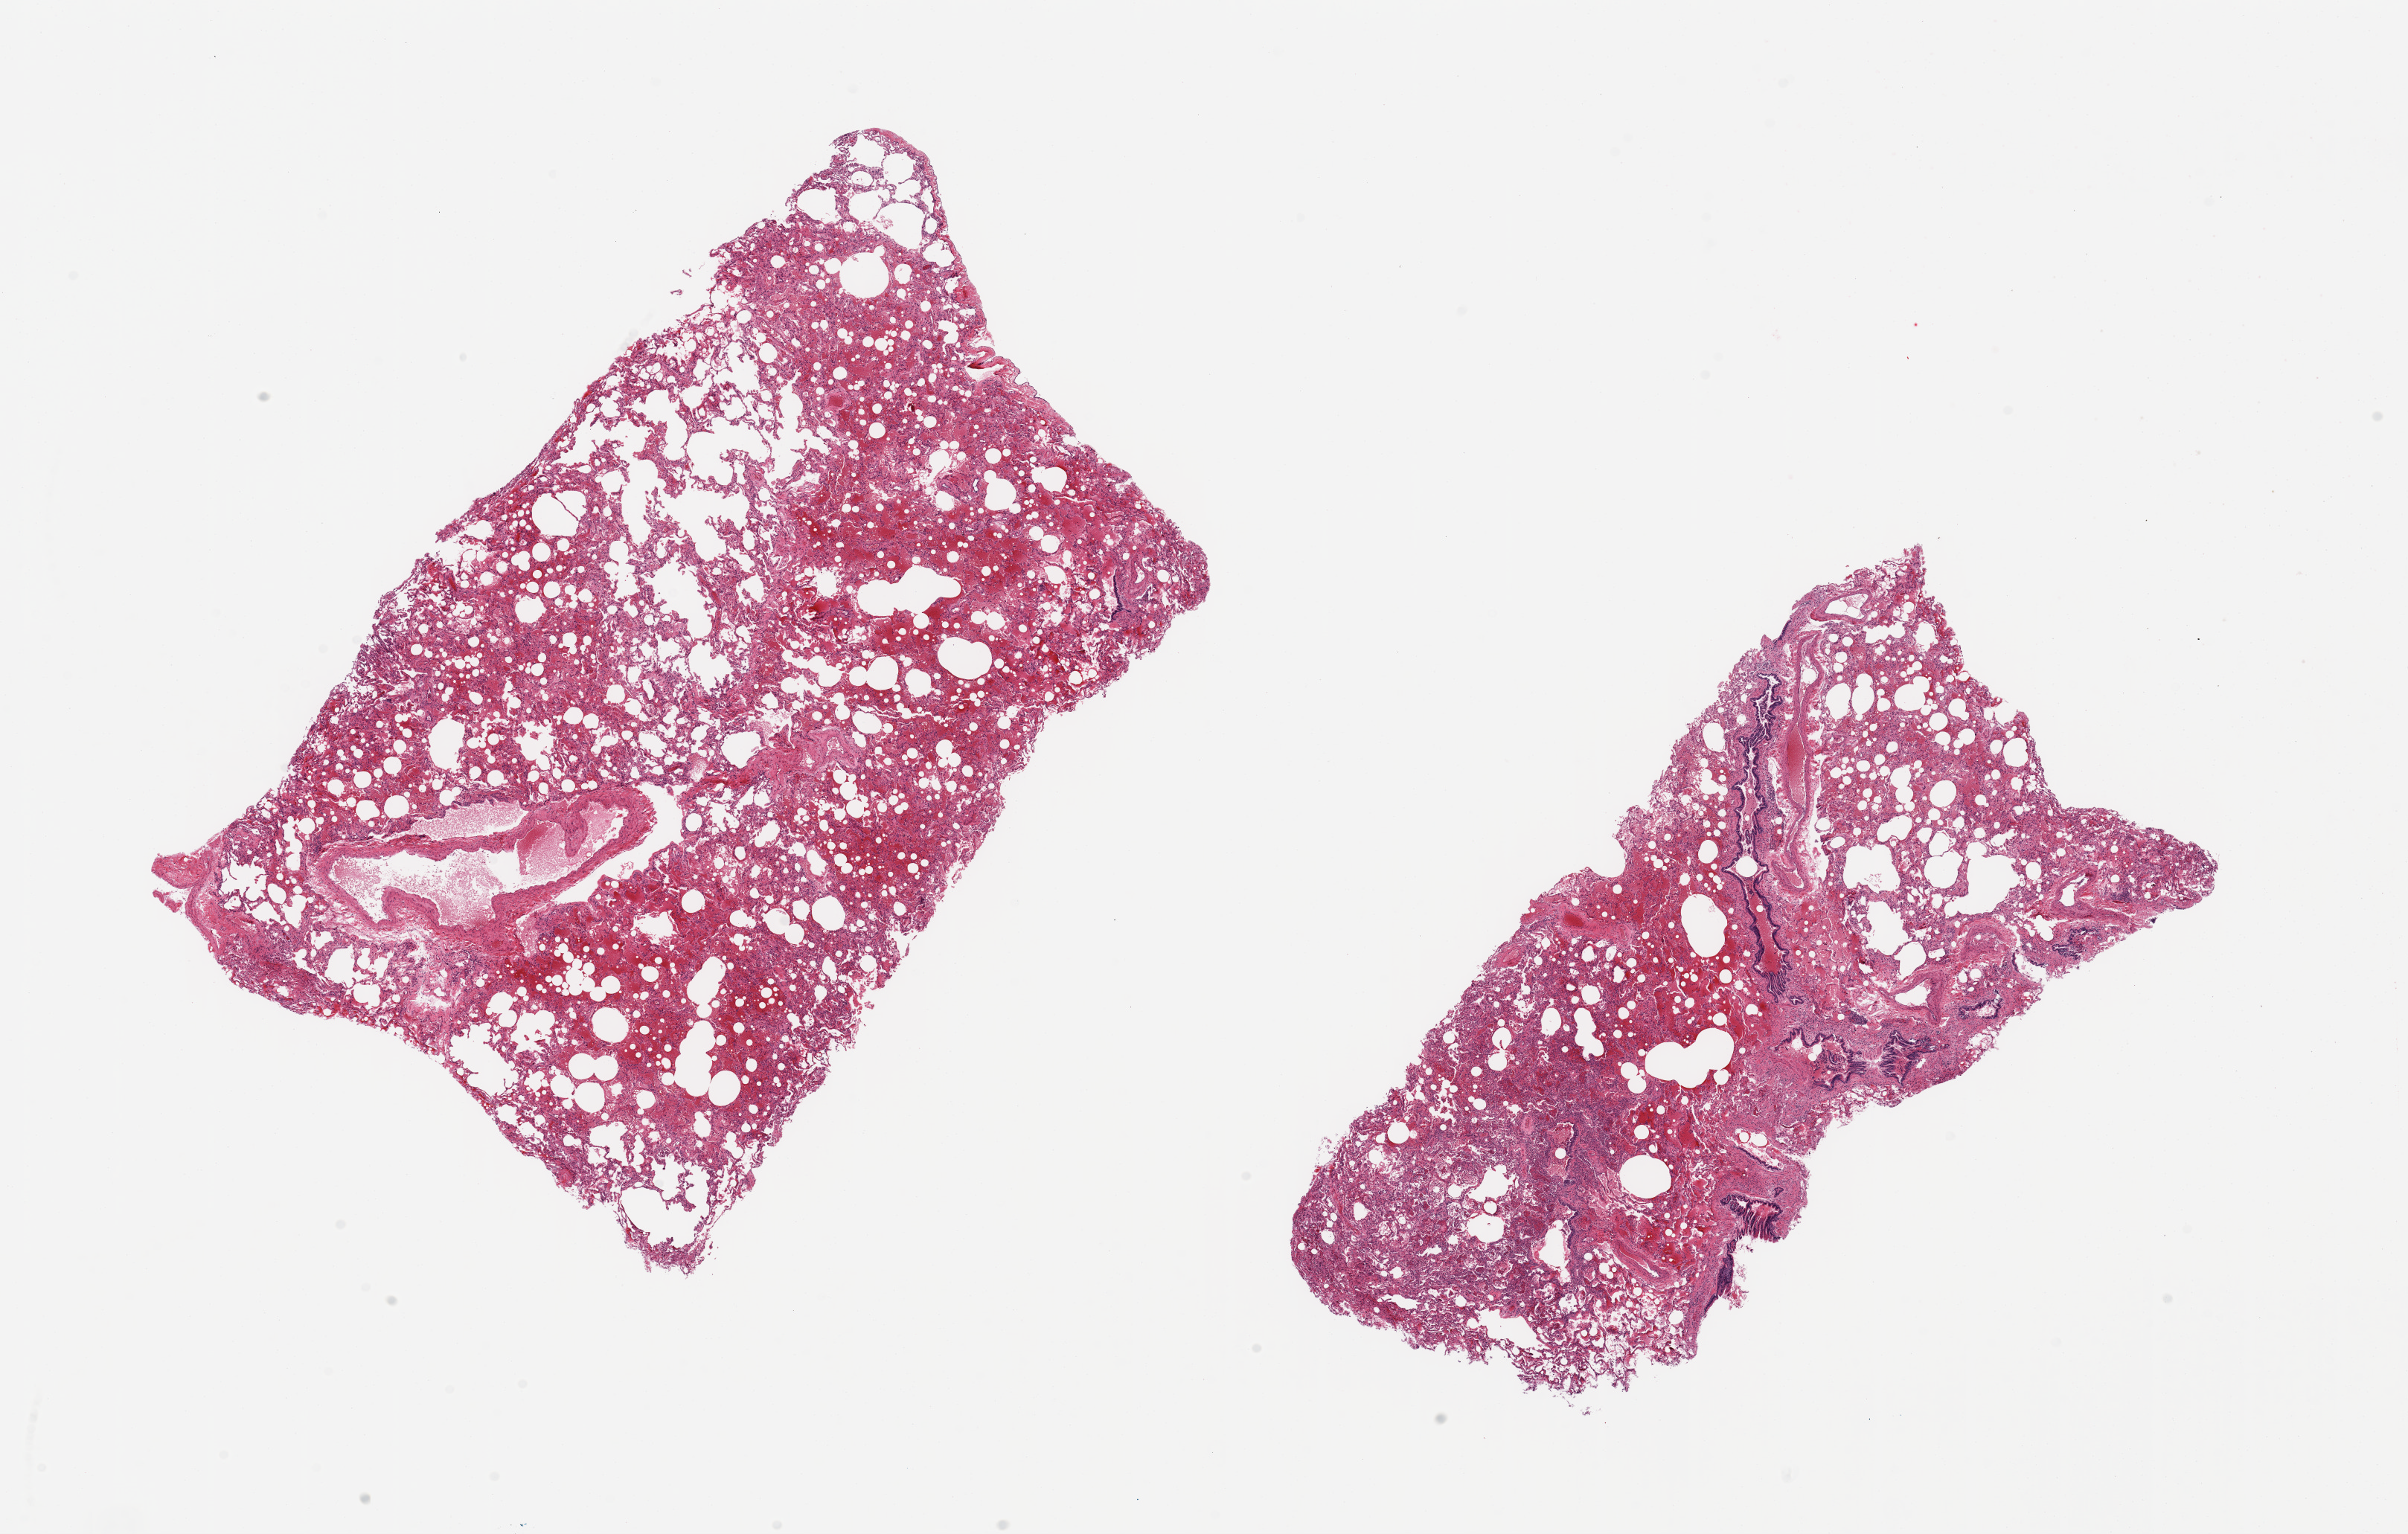
Whole-slide image, haematoxylin and eosin stain, whole scanned area (about 25.6 x 16.3 mm) shown as a low-resolution overview, PAXgene-fixed, paraffin-embedded tissue, section of lung (target tissue), tissue donor sample. Donor sex: male.
- pathologist's review note for this sample: 2 ~9x 6mm pieces. Moderate congestion